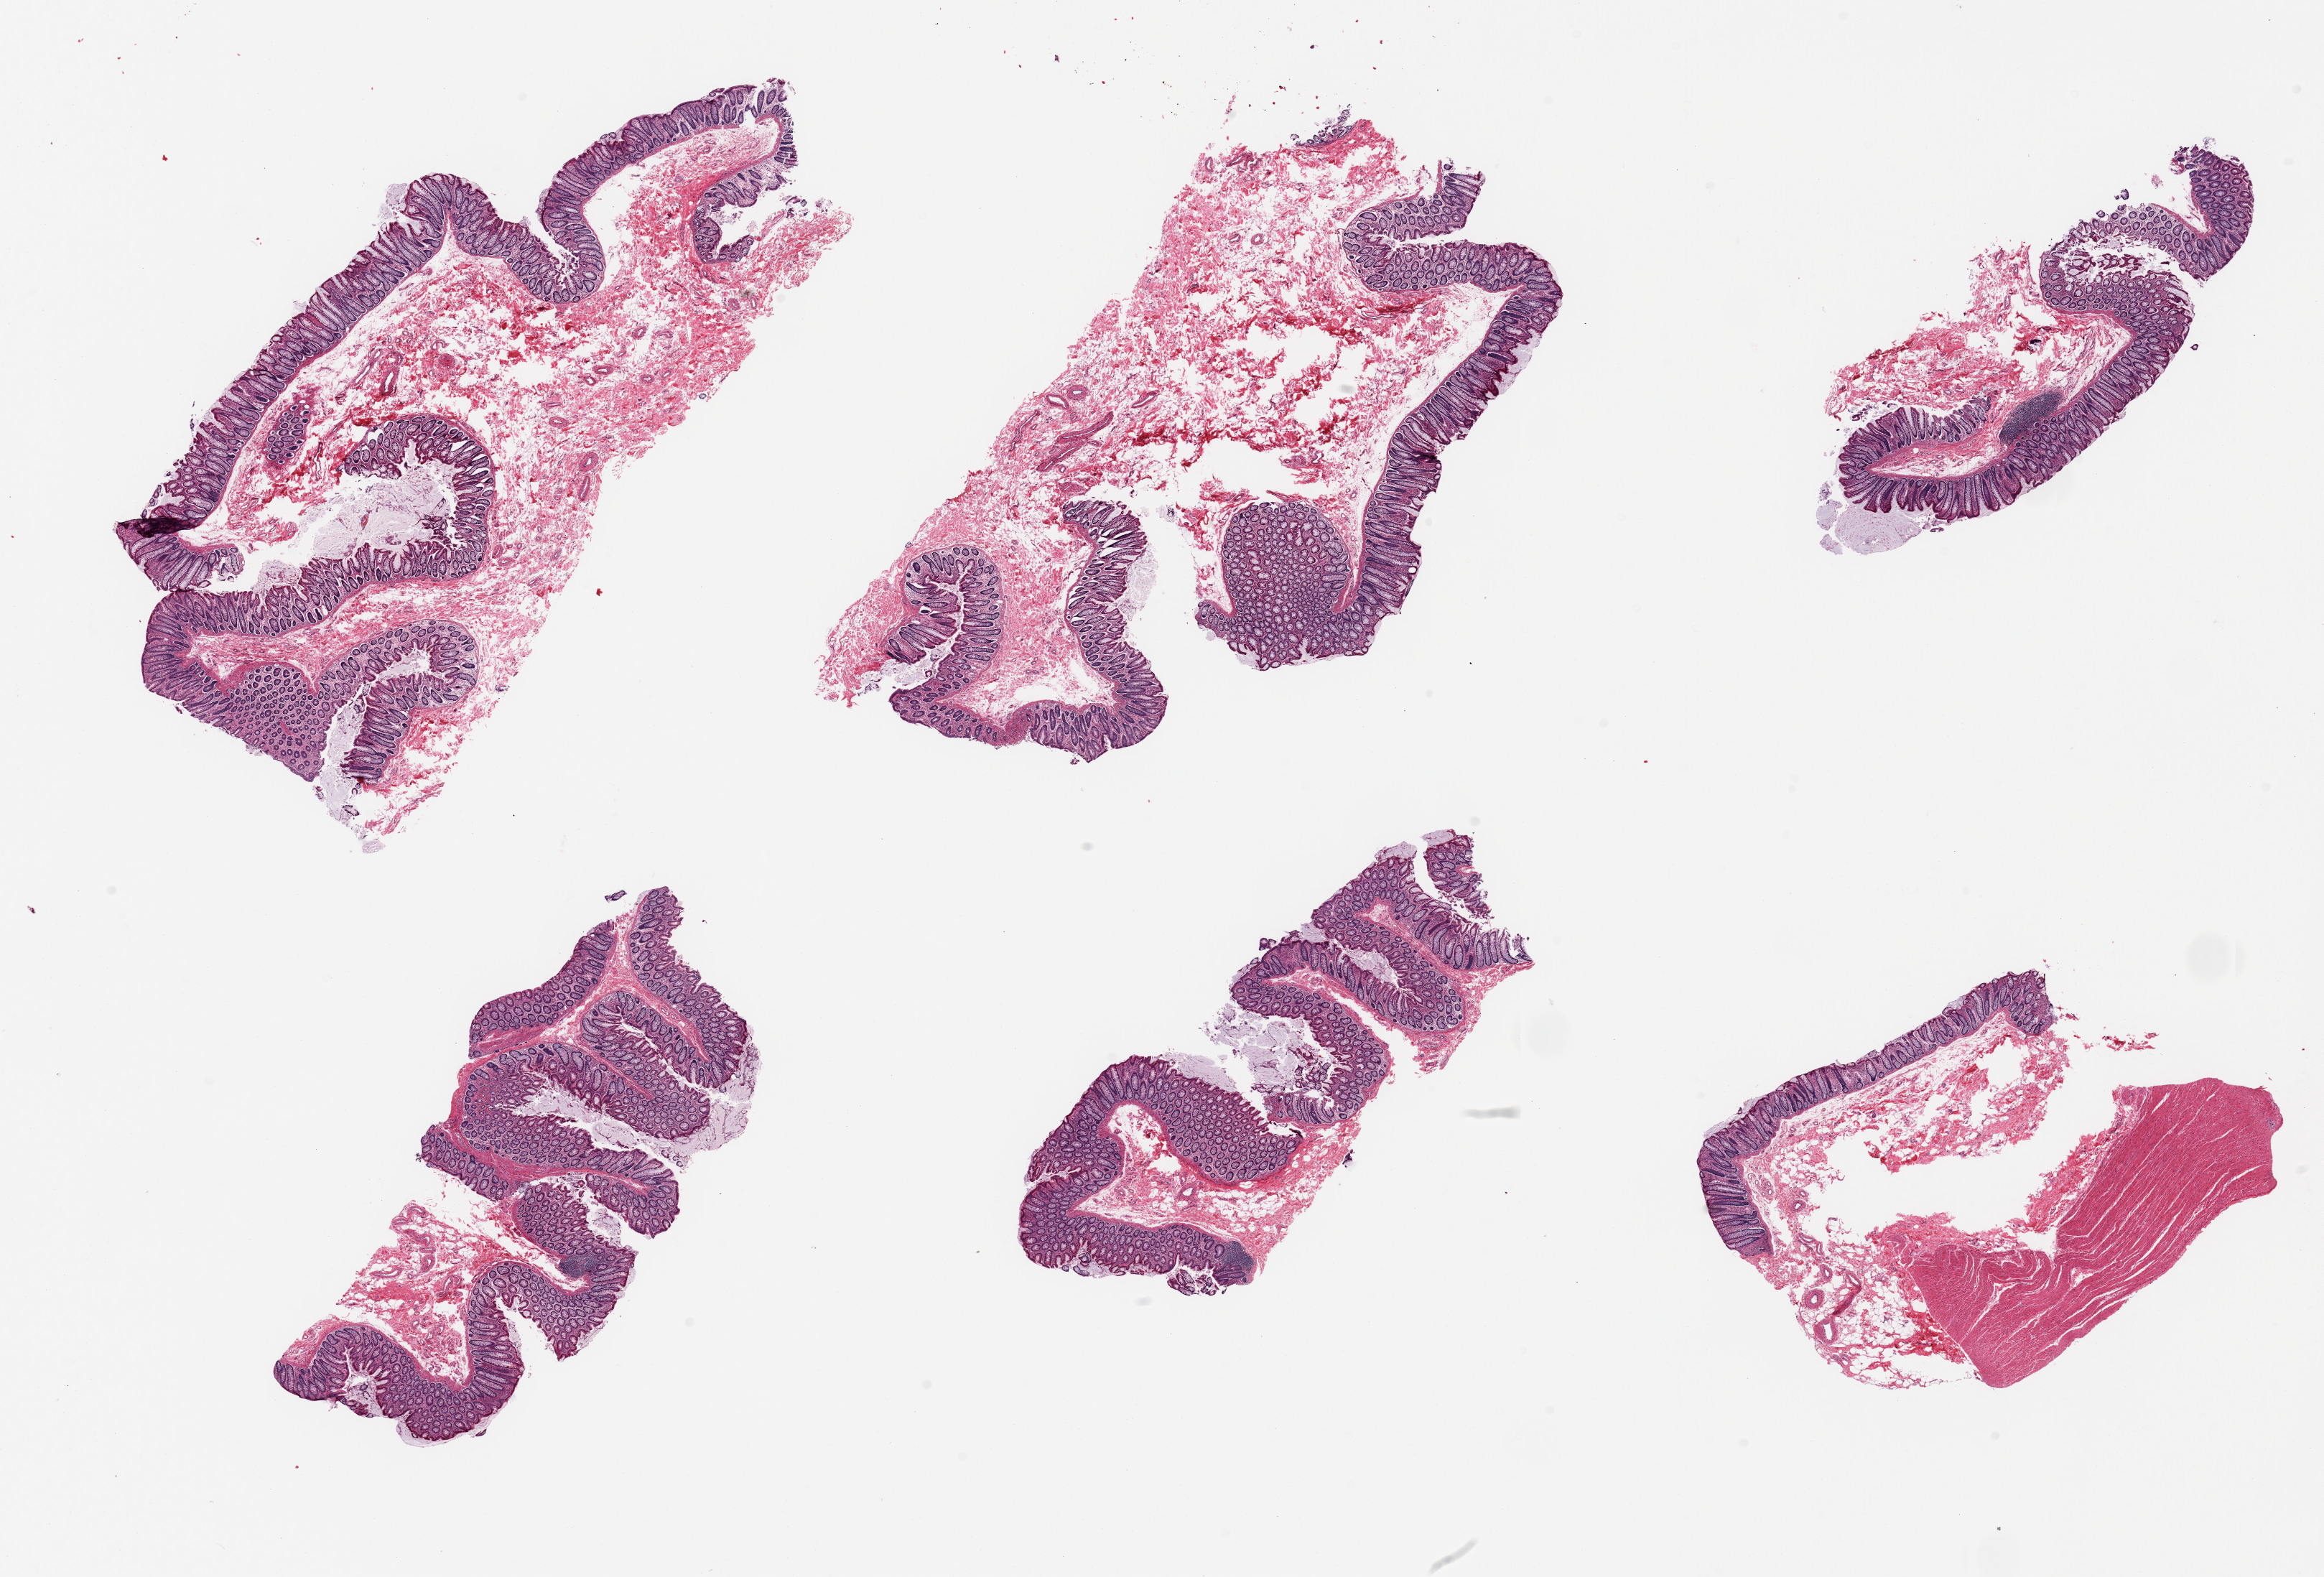
Digitized H&E-stained section, low-resolution overview of the scanned area, about 25.6 x 17.4 mm. PAXgene-fixed paraffin-embedded (PFPE) section. Target tissue: transverse colon. Donor tissue sample. Male donor.
- review note (as recorded): 6 pieces; 1 of 6 includes portion of muscularis (not target)